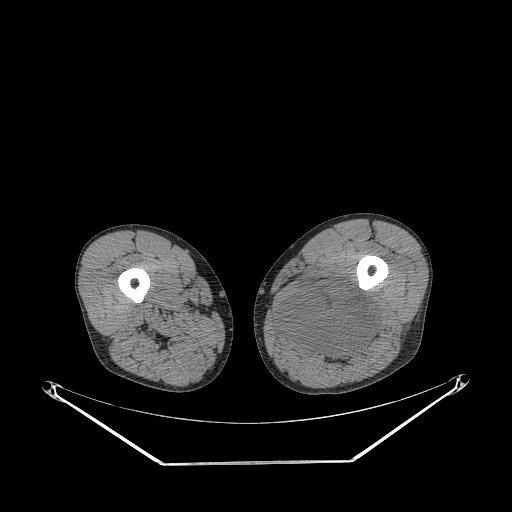
CT of an extremity soft-tissue mass (from a PET/CT study), one axial slice; slice 240 of 267 in the series (ordered by position); reconstruction kernel STANDARD; soft-tissue window (W 400 / L 40 HU); 3.75 mm slice thickness; 512 × 512 image matrix, field of view 500 × 500 mm. Male patient. Case-level facts recorded for this patient, not image findings: histological type: undifferentiated pleomorphic liposarcoma; grade: high; site of the primary tumour: left thigh.
Structures marked on this image (expert contour drawn on MRI and transferred to this co-registered scan by the dataset authors):
- gross tumour volume including surrounding oedema: bounding box <279,283,376,362> (left, top, right, bottom; pixels)
- gross tumour volume (mass): <279,283,376,357>